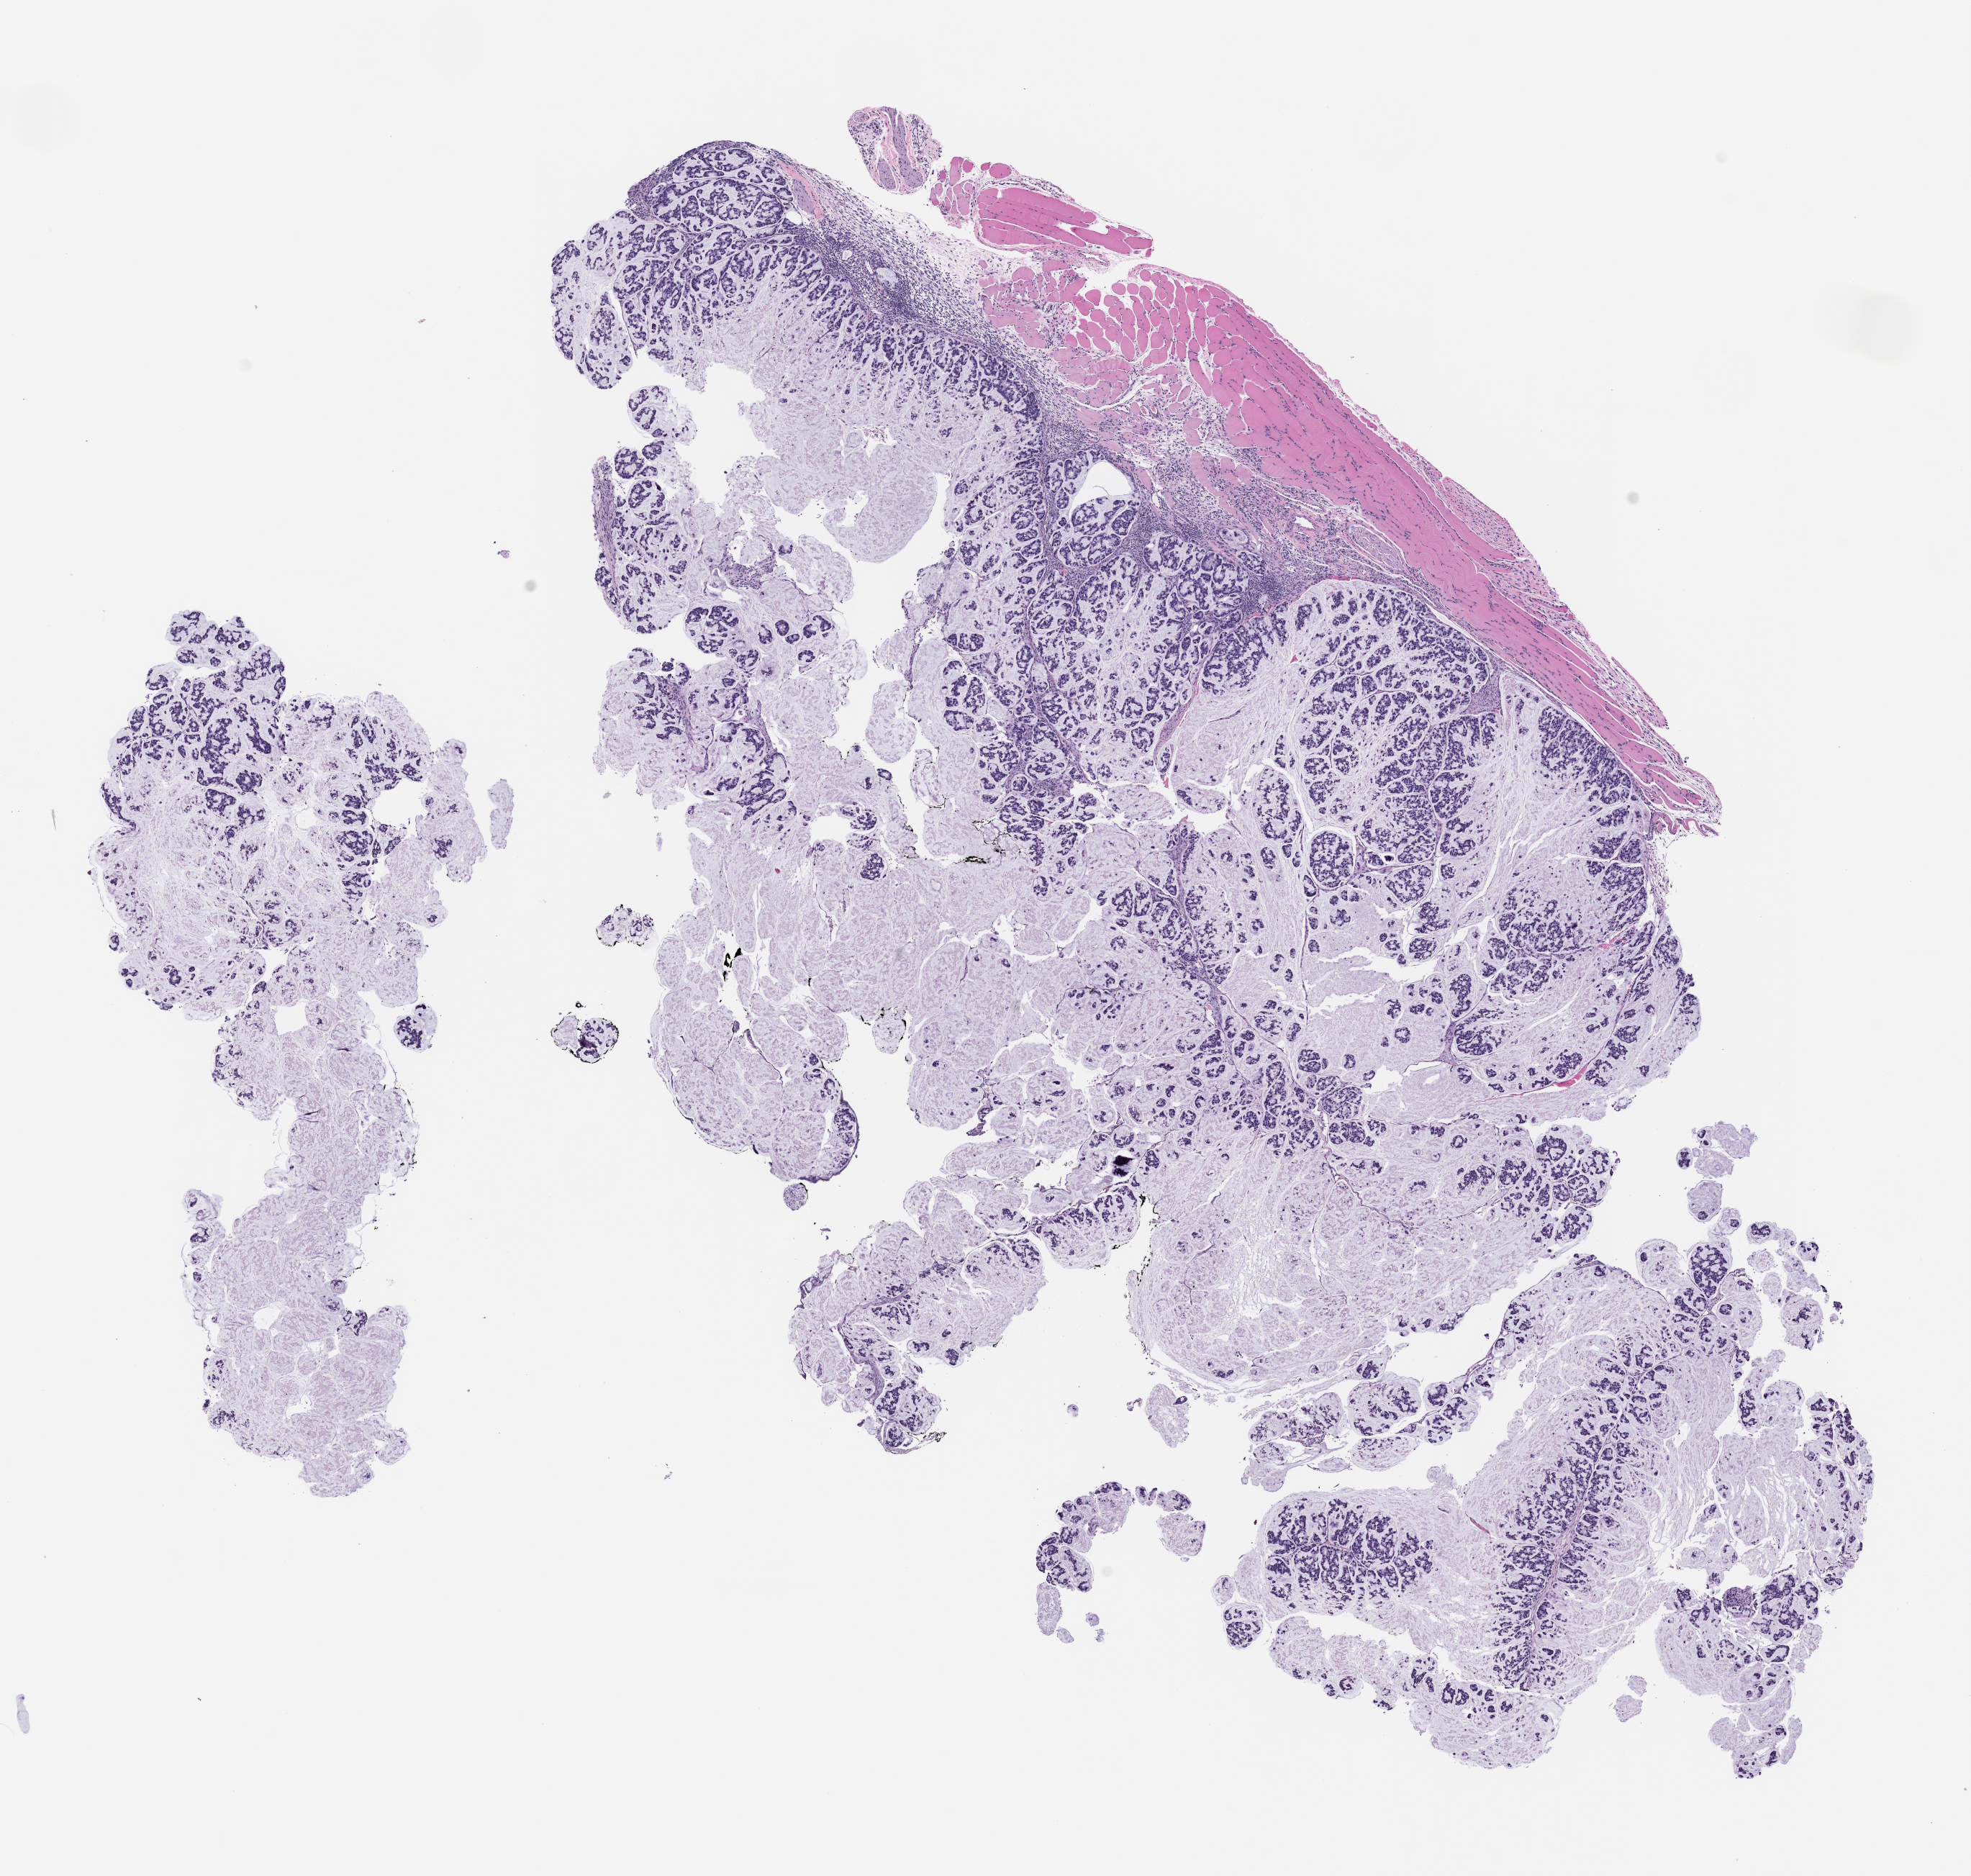
Whole-slide image, hematoxylin and eosin (H&E): patient-derived xenograft (human tumor grown in a mouse), passage 2 — whole scanned area (about 11.0 x 10.5 mm) shown as a low-resolution overview; formalin-fixed paraffin-embedded section; originating tumor site category: colon.
Originating patient diagnosis: Colon Adenocarcinoma.